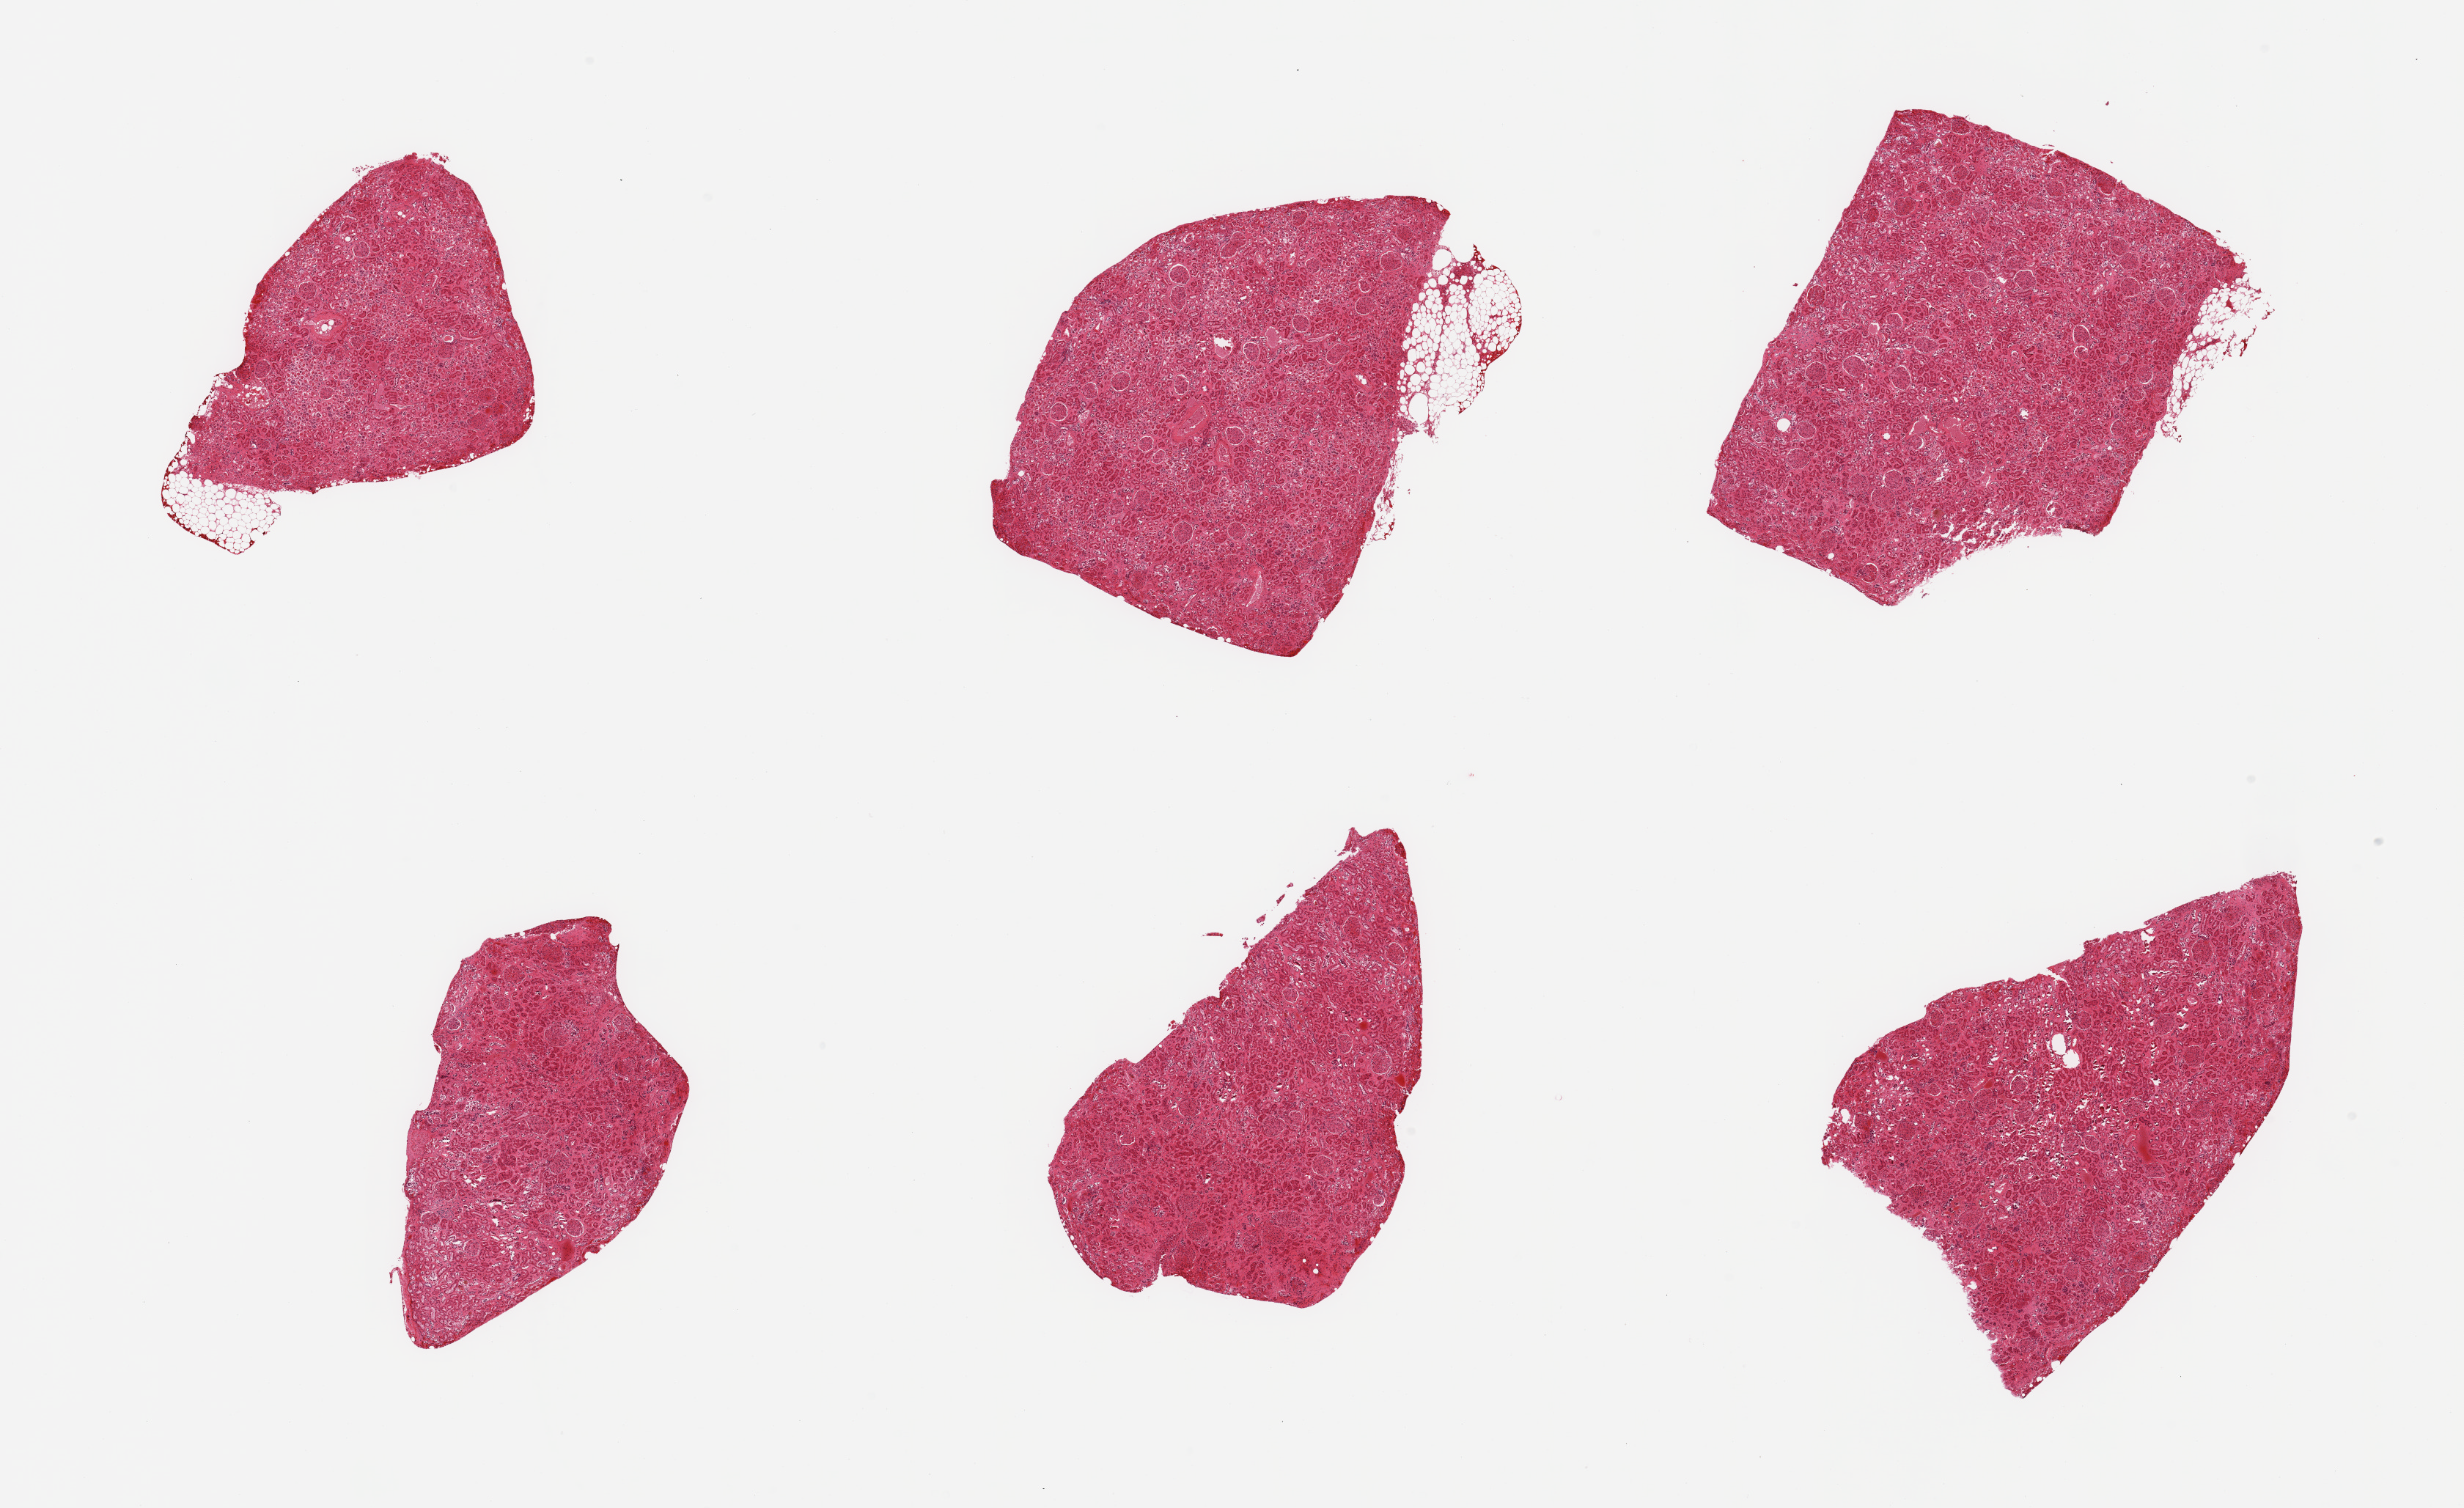
Digitized hematoxylin and eosin (H&E)-stained section, whole scanned area (about 26.6 x 16.3 mm) shown as a low-resolution overview; PAXgene-fixed paraffin-embedded (PFPE) section; target tissue: renal cortex; donor tissue sample. Donor: male.
Reviewer comment on this tissue sample: 6 pieces; congested renal cortex, arteriosclerosis, small amount of fat attached to 3 of 6 pieces.